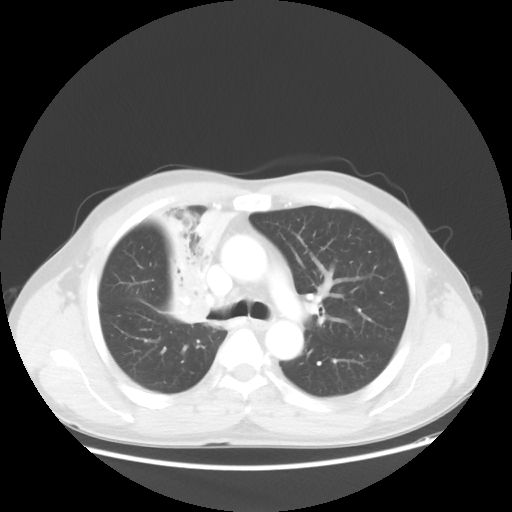
Chest CT, one axial slice. Reconstruction kernel STANDARD. Lung window (W 1500 / L -600 HU). 5 mm slice thickness. 512 × 512 image matrix. Male patient, age 60 years. Case-level facts recorded for this patient, not image findings: clinical TNM (as recorded): T2a N1 M0.
Structures marked on this image (rectangle marked by the reading radiologist):
- lung tumour (recorded histology: squamous cell carcinoma): box from (x=146, y=197) to (x=231, y=328) px